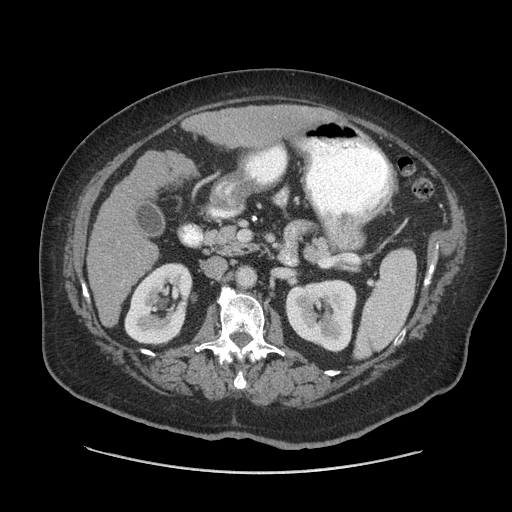
Contrast-enhanced abdominal CT (liver protocol), one axial slice; slice 26 of 91 in the series (ordered by position); soft-tissue window (W 400 / L 40 HU); 2.5 mm slice thickness; 512 × 512 image matrix. From the clinical record (not read from this slice): diagnosis: hepatocellular carcinoma (patient treated with transarterial chemoembolisation; whether this scan precedes or follows treatment is not stated here); TNM stage (as recorded): Stage-I; Child-Pugh class: A; tumour differentiation: well differentiated; tumour nodularity: uninodular.
Annotated regions visible in this slice (semi-automatically segmented with operator editing):
- liver parenchyma outside the tumour (the mass and vessels are separate outlines, so this box may not span the whole liver): bounding box <86,104,326,326> (left, top, right, bottom; pixels)